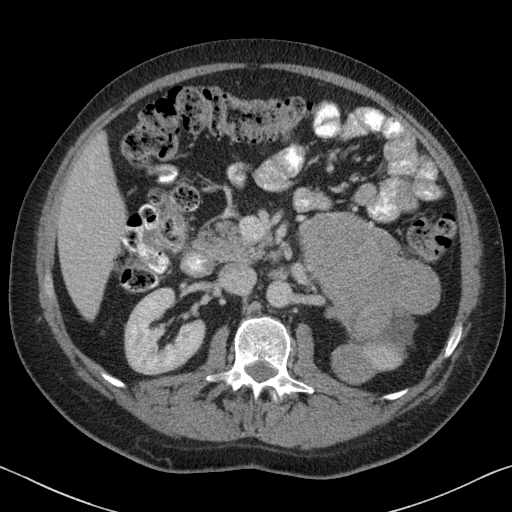
Contrast-enhanced abdominal CT, one axial slice; position 37 of 88 along the scan axis; reconstruction kernel B31f; 120 kVp; soft-tissue window (W 400 / L 40 HU); 3 mm slice thickness; 512 × 512 image matrix. Patient: male, 51 years. From the clinical record (not read from this slice): diagnosis: adrenocortical carcinoma; tumour side: left adrenal; tumour size at pathology: 16.5 cm; Ki-67 index: 30 %; stage (as recorded): 2.
Annotated regions visible in this slice (semi-automatic segmentation, software-assisted and operator-edited):
- mass: bounding box (x1, y1, x2, y2) in pixels: (303, 215, 441, 382)